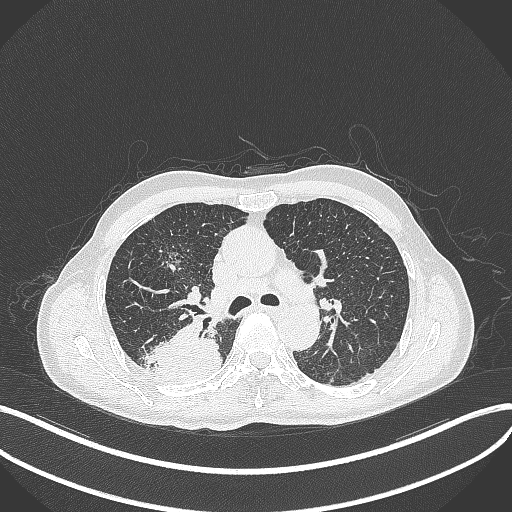
Chest CT, one axial slice; reconstruction kernel B70f; 120 kVp; lung window (W 1500 / L -600 HU); 1 mm slice thickness; 512 × 512 image matrix, field of view 400 × 400 mm. Patient: male, 79 years. Case-level facts recorded for this patient, not image findings: clinical TNM (as recorded): T3 N0 M0.
Annotated regions visible in this slice (rectangle marked by the reading radiologist):
- lung tumour (recorded histology: adenocarcinoma): bounding box (x1, y1, x2, y2) in pixels: (150, 320, 224, 383)